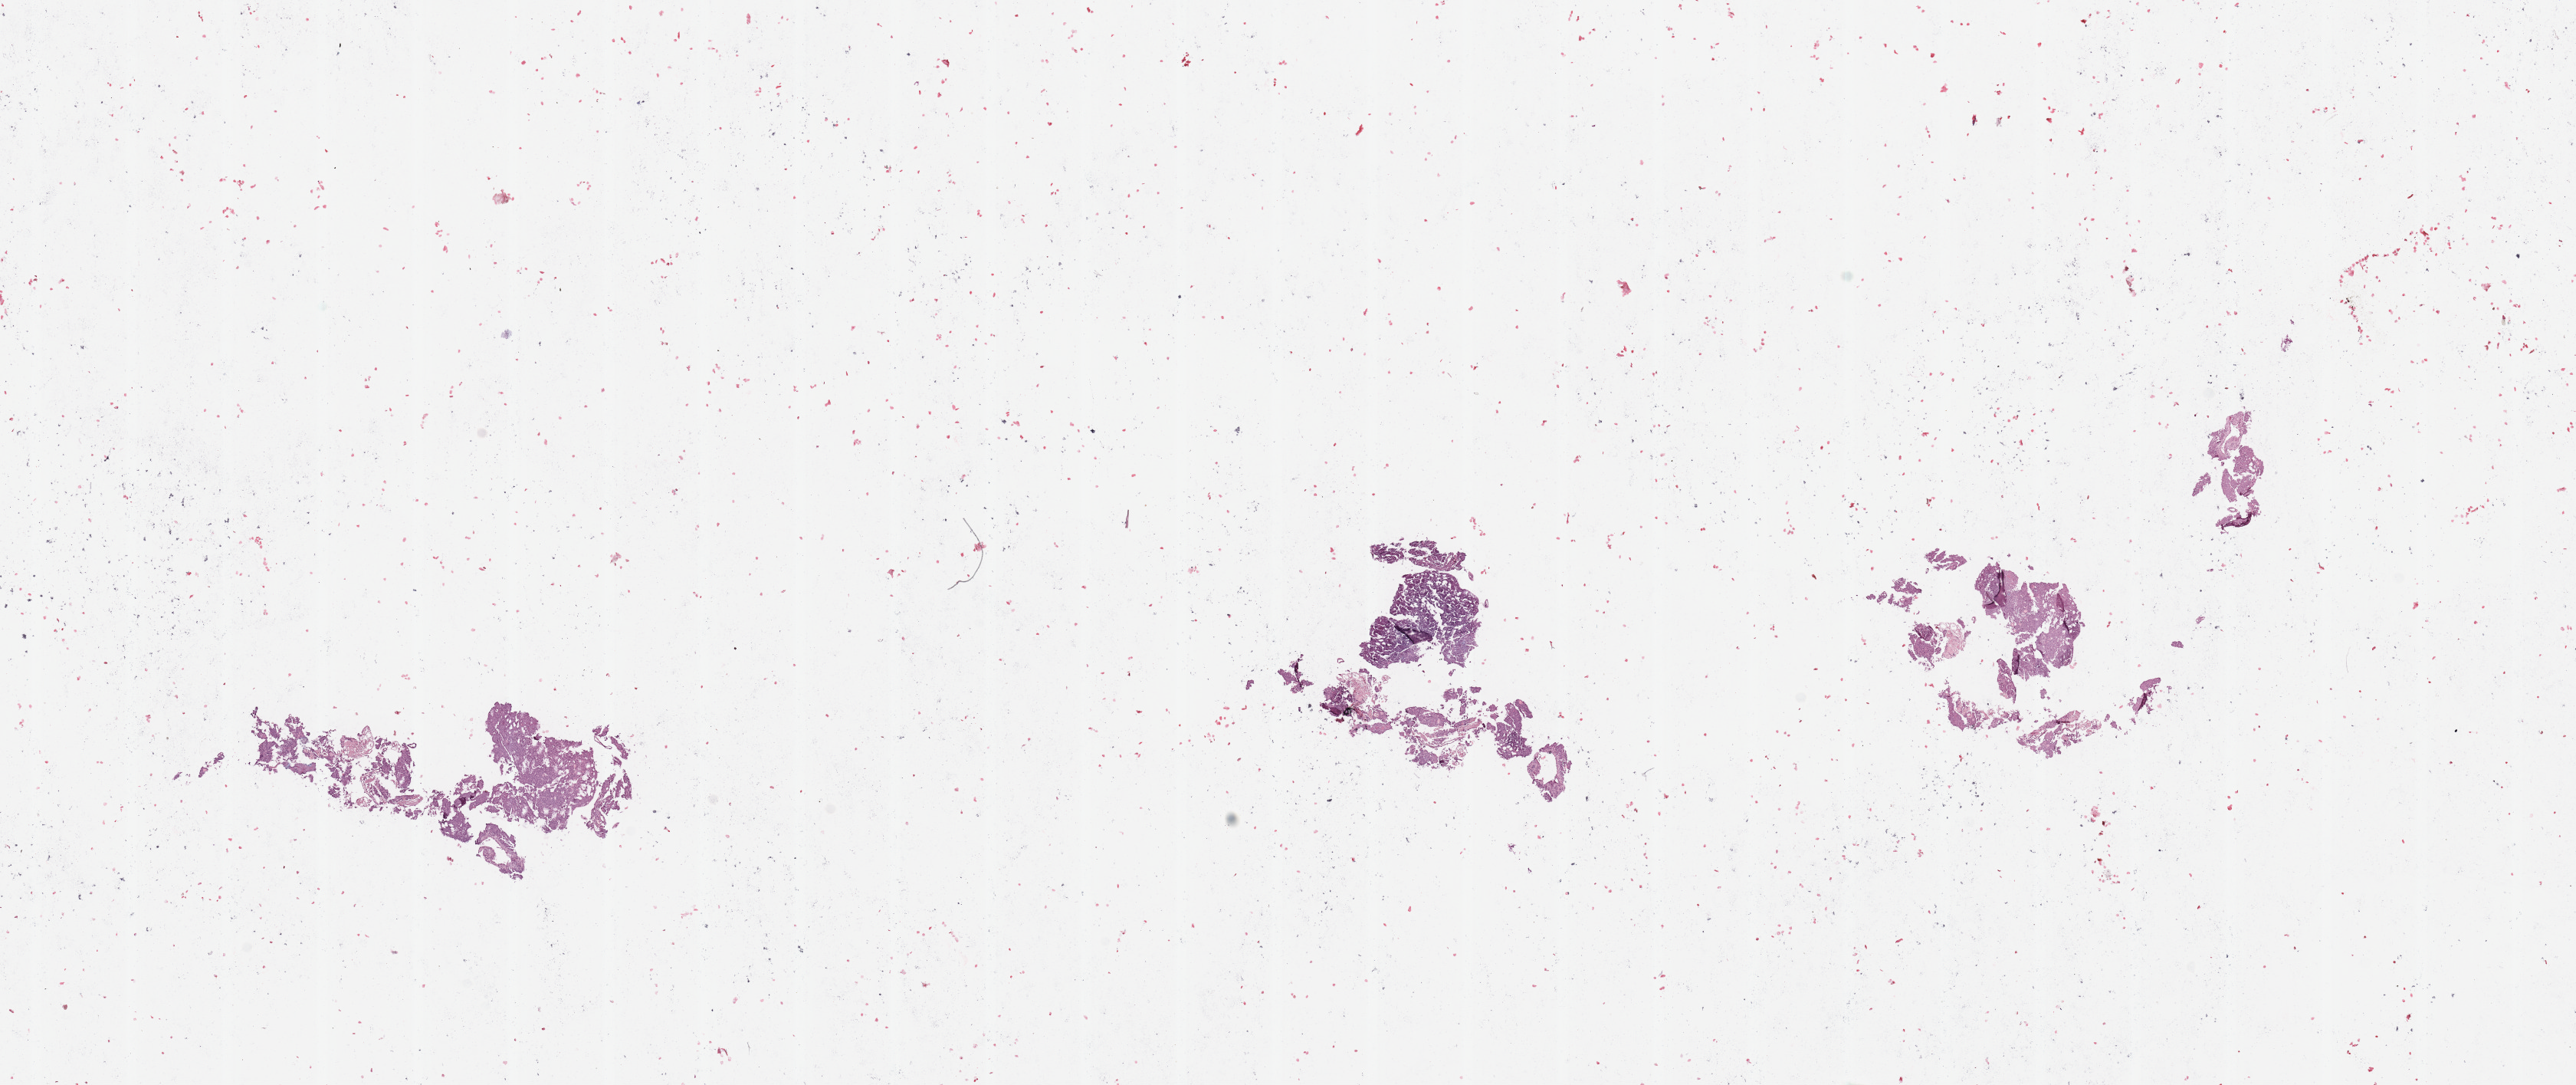
Hematoxylin and eosin (H&E) stained whole-slide image — shown as a low-resolution overview of the whole scanned area (about 26.6 x 11.2 mm, slide scanned at 20x). Tumour tissue sample, sampled site: uterus. 77-year-old female patient. Composition of this section per pathologist review: tumour nuclei 90%, necrosis 2%.
Diagnosis: Endometrioid adenocarcinoma, NOS.